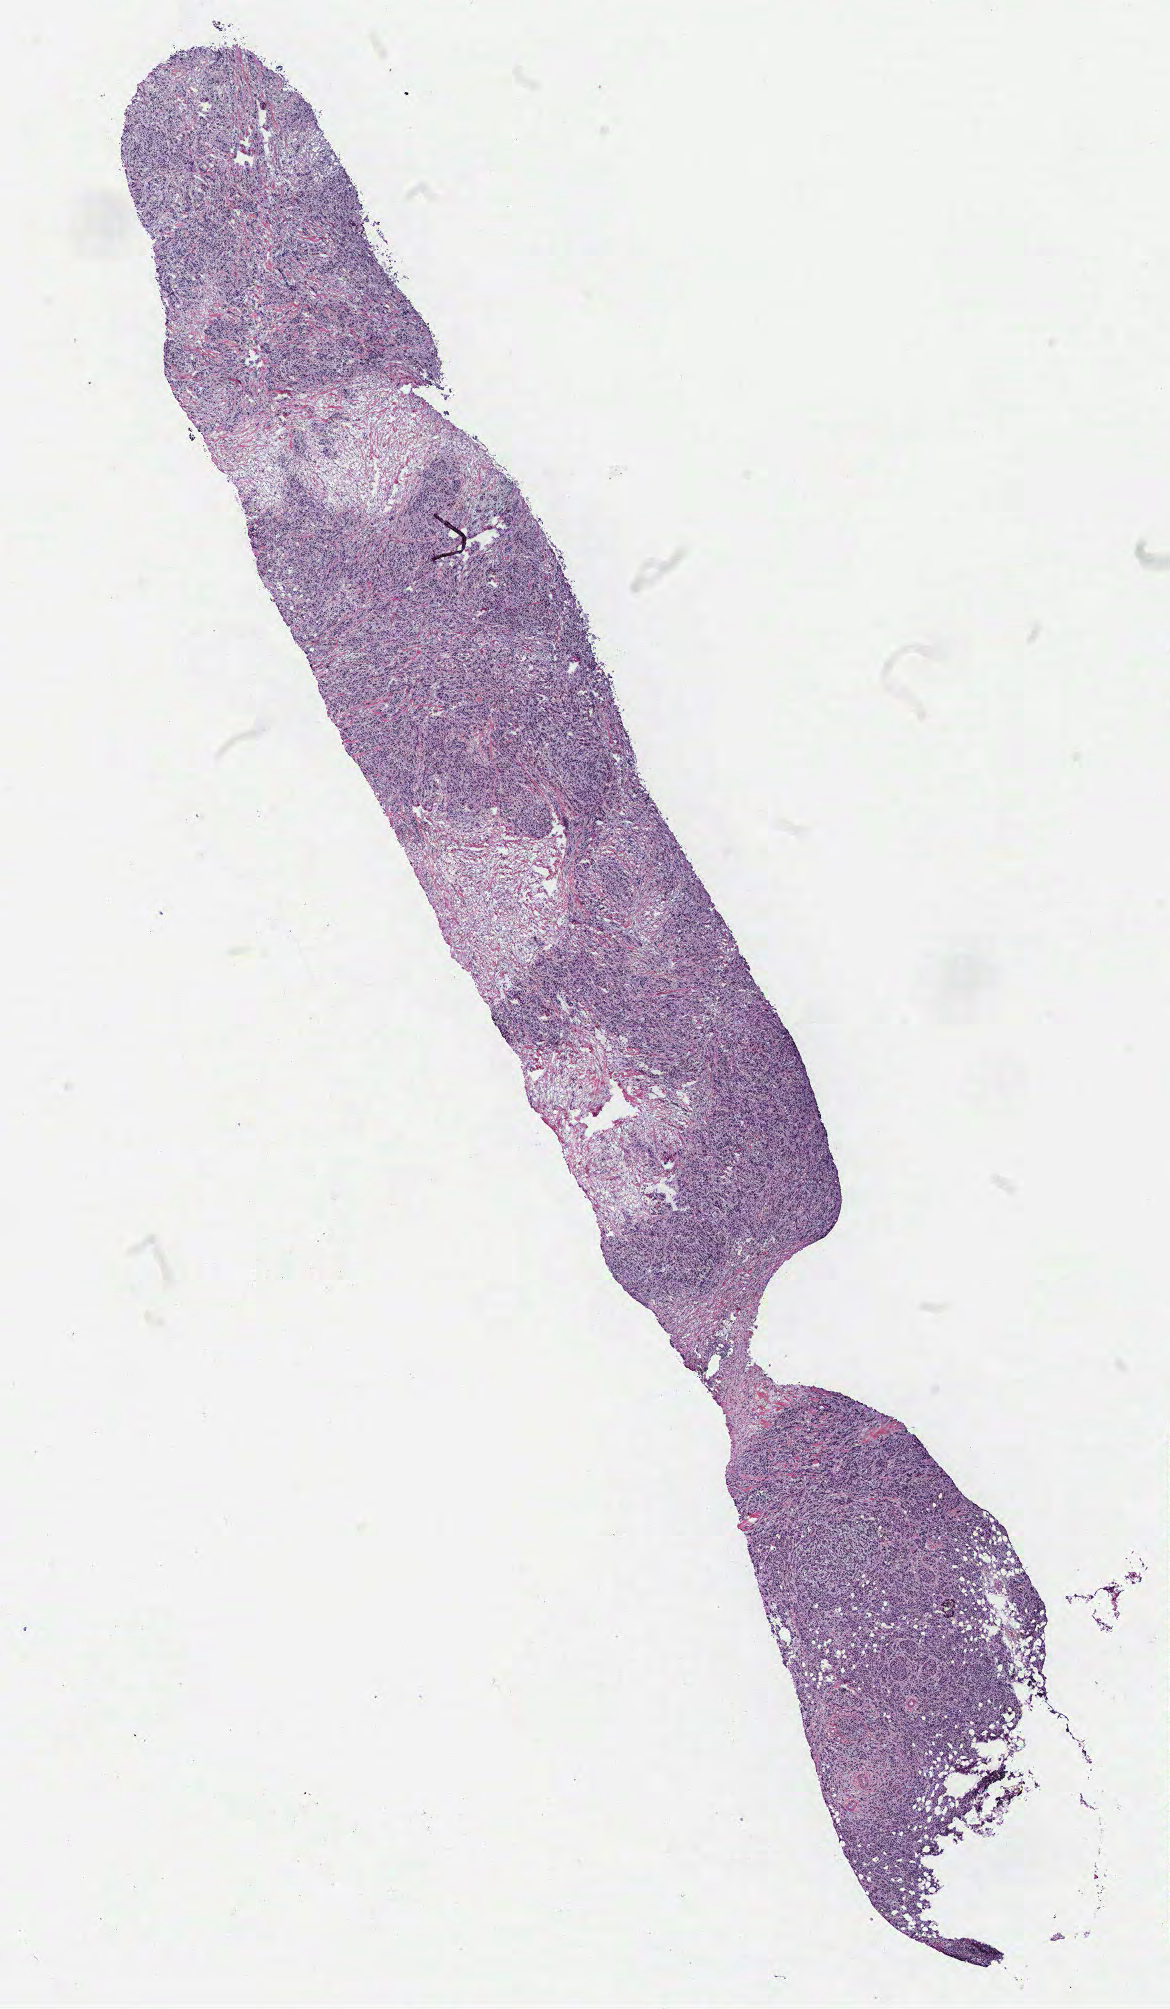
Digitized Hematoxylin and eosin (H&E) stained tissue section (whole slide), whole scanned area (about 9.4 x 16.1 mm, slide scanned at 40x) shown as a low-resolution overview, breast, tissue type not recorded.
Patient diagnosis (cohort enrolment): breast cancer (breast).